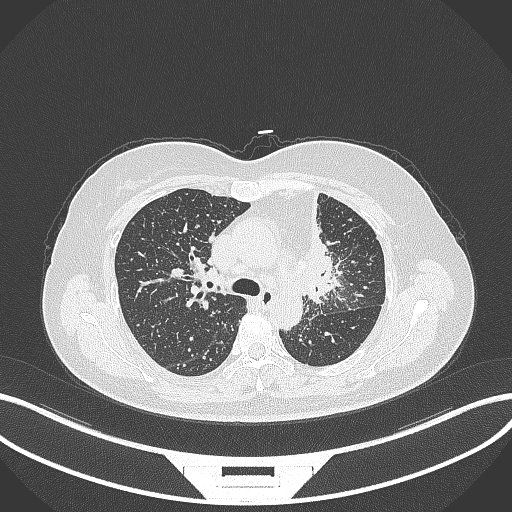
Chest CT, one axial slice. Reconstruction kernel B70f. Lung window (W 1500 / L -600 HU). 1 mm slice thickness. 512 × 512 image matrix, field of view 400 × 400 mm. Patient: female, 49 years. From the clinical record (not read from this slice): clinical TNM (as recorded): T1c N0 M1.
Annotated regions visible in this slice (rectangle marked by the reading radiologist):
- lung tumour (recorded histology: adenocarcinoma): bounding box (x1, y1, x2, y2) in pixels: (292, 191, 345, 311)